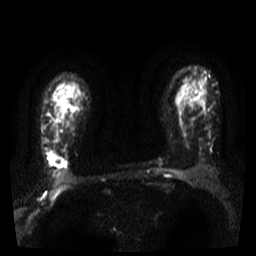
Breast MRI, one axial slice; position 27 of 36 along the scan axis; diffusion-weighted series; image 2 of 4 stored at this slice position (different b-values; order by instance number); 3 T; 5 mm slice thickness; 256 × 256 image matrix. Female patient.
Annotated regions visible in this slice (expert manual segmentation):
- tumour on diffusion-weighted imaging: bounding box (x1, y1, x2, y2) in pixels: (49, 155, 55, 164)